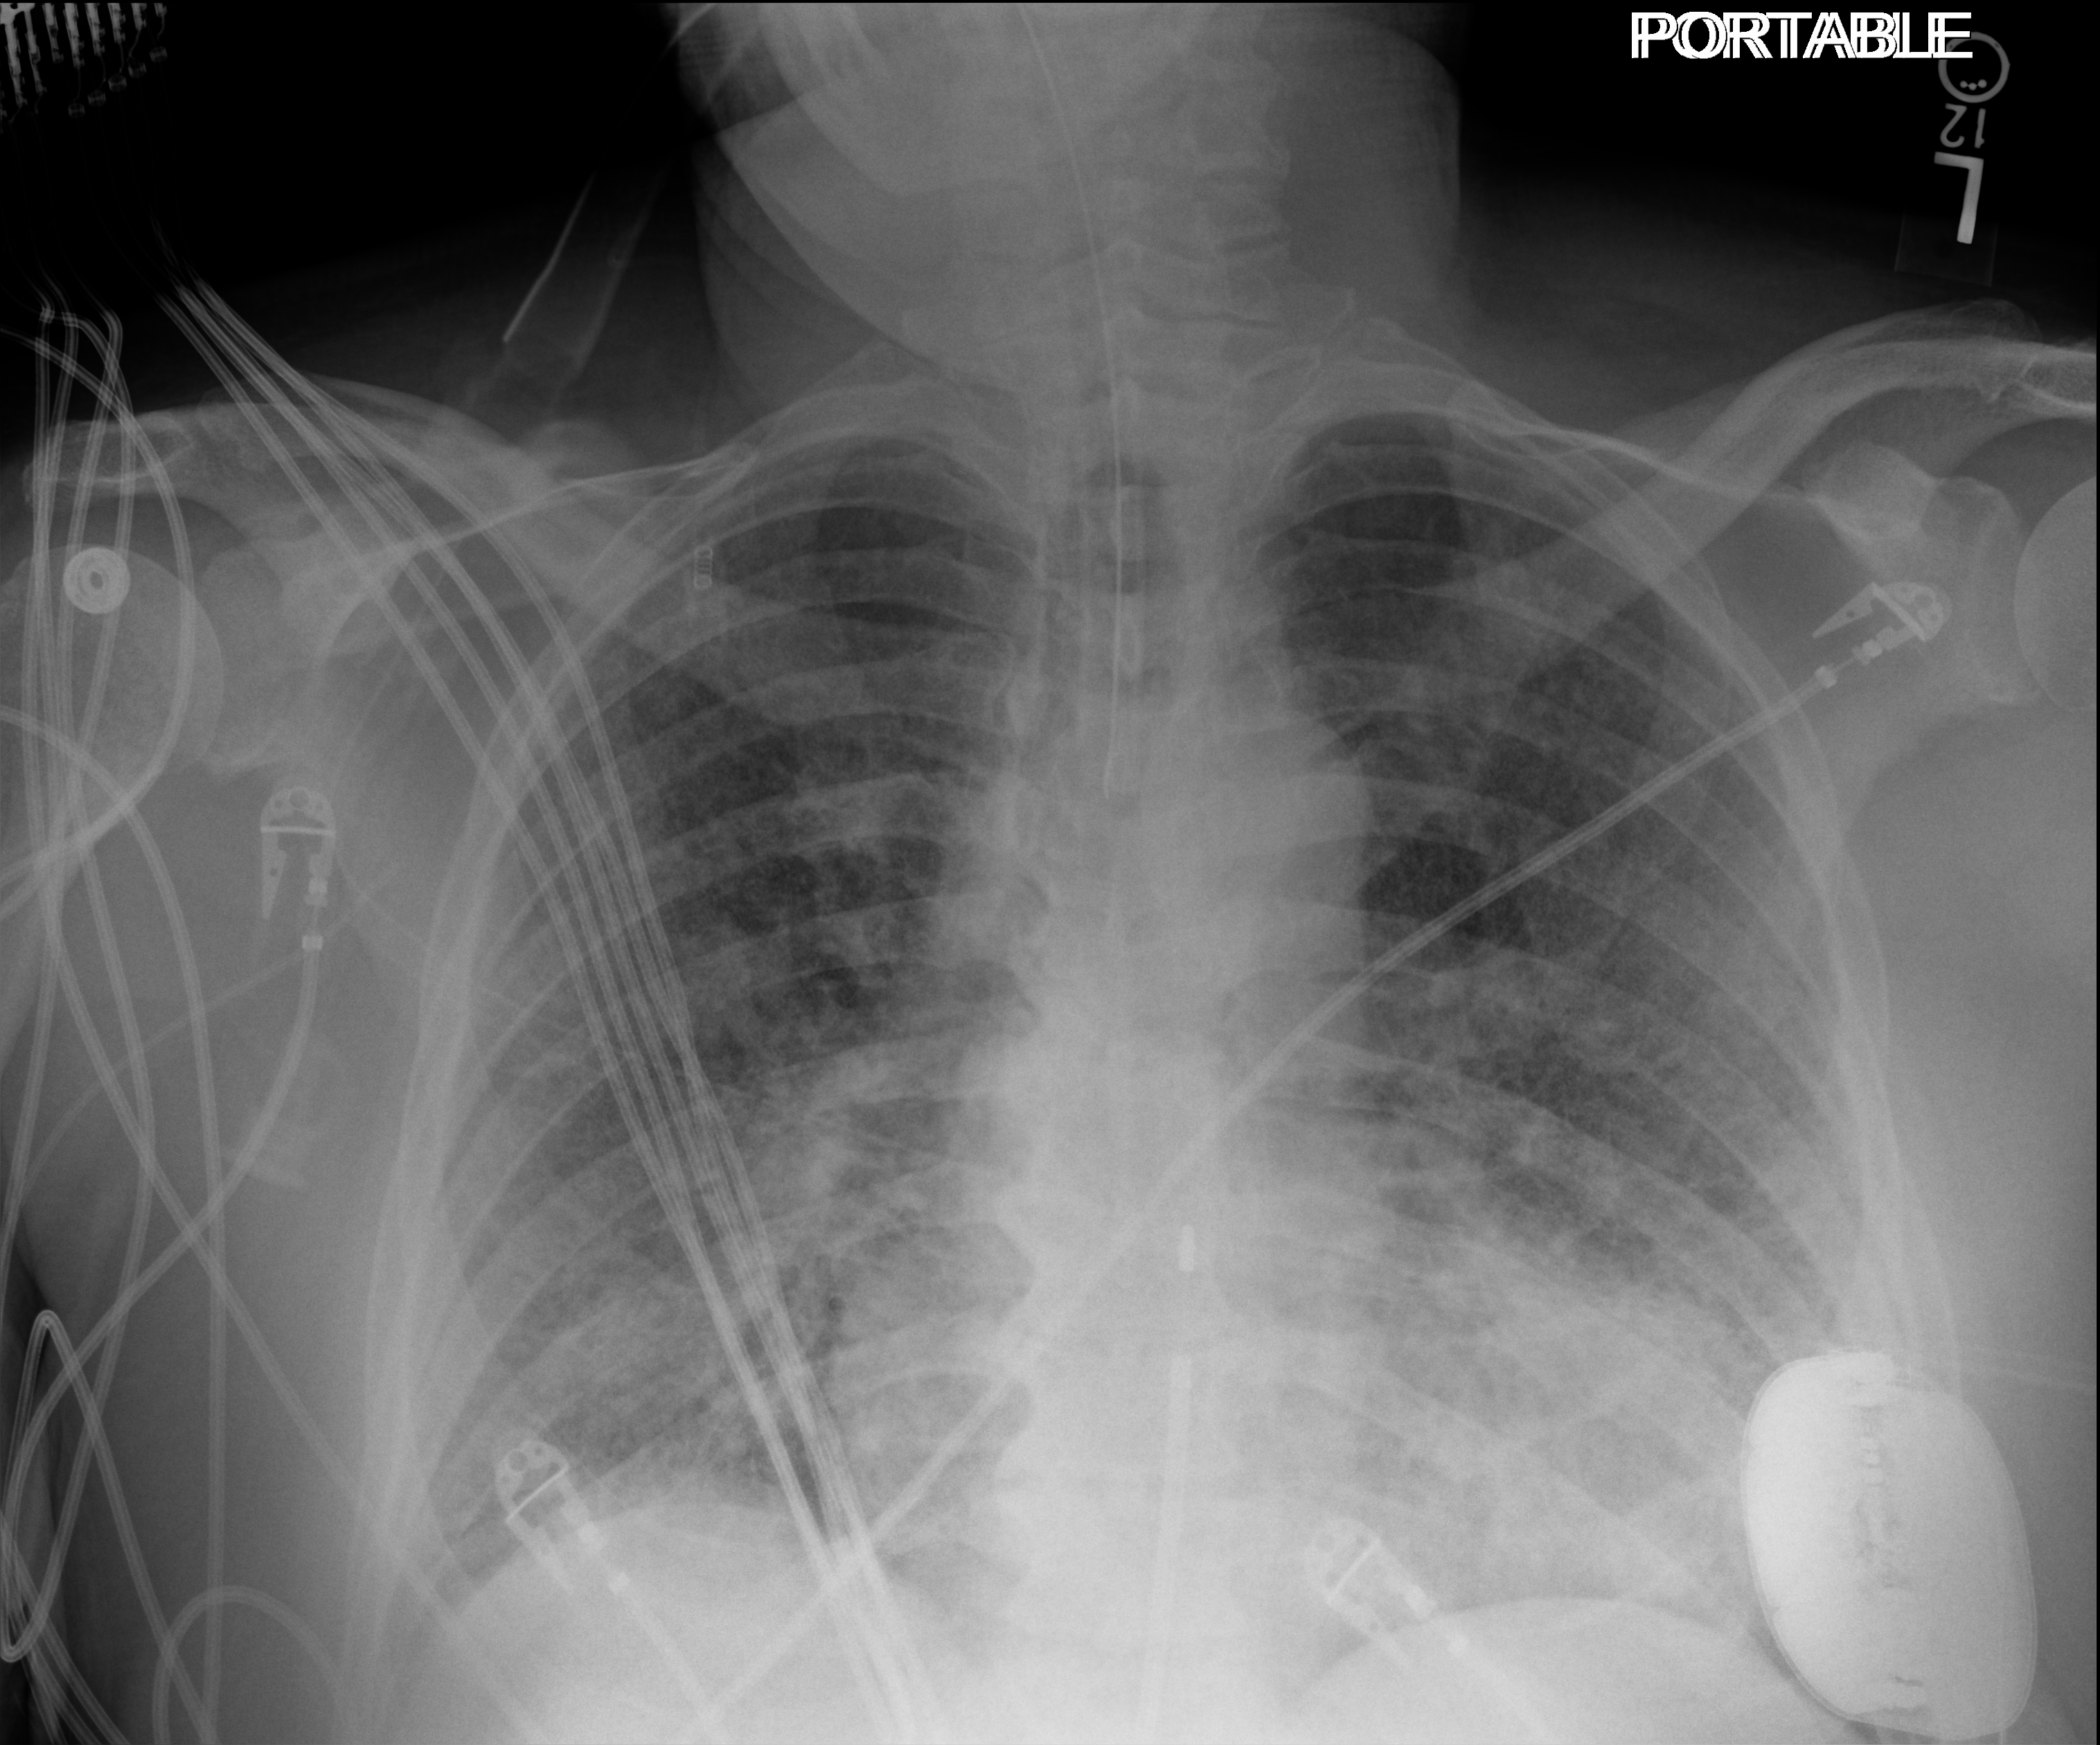
Portable chest radiograph, anteroposterior (AP) projection. Male patient hospitalised with COVID-19, age 60–74 years.
Hospital-stay facts (about this admission, not read from this image; timing relative to this image not recorded): admitted to intensive care during this hospital stay: yes; hypertension (admission record): yes; COPD (admission record): no.